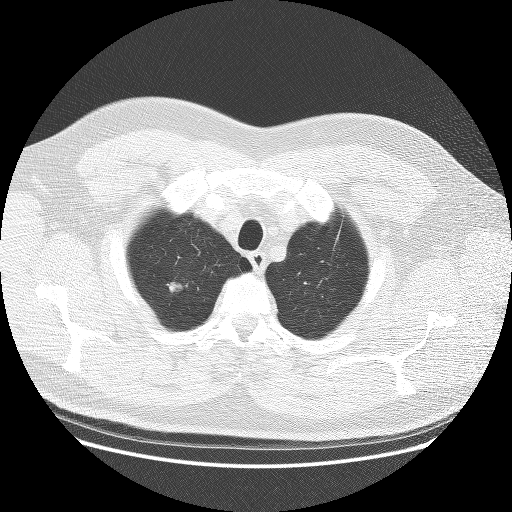
Low-dose screening chest CT, axial slice. Baseline screening round. Lung window (W 1500 / L -600 HU). Lung (sharp) reconstruction kernel (BONE). Slice 15 of 111 in the series. 512 × 512 image matrix. Male participant, aged 65 years at enrolment.
Expert-annotated lung lesion, bounding box (x1, y1, x2, y2) in pixels: (148, 266, 205, 314). Reader record for this screening exam (exam-level; its link to the box is not recorded): non-calcified nodule or mass ≥4 mm, right upper lobe, 11 × 9 mm, poorly defined margins, soft tissue attenuation. Participant outcome: lung cancer diagnosed 44 days after this screen — adenocarcinoma, NOS, right upper lobe, moderately differentiated (G2), stage IA (AJCC 6th edition), 11 mm at pathology.